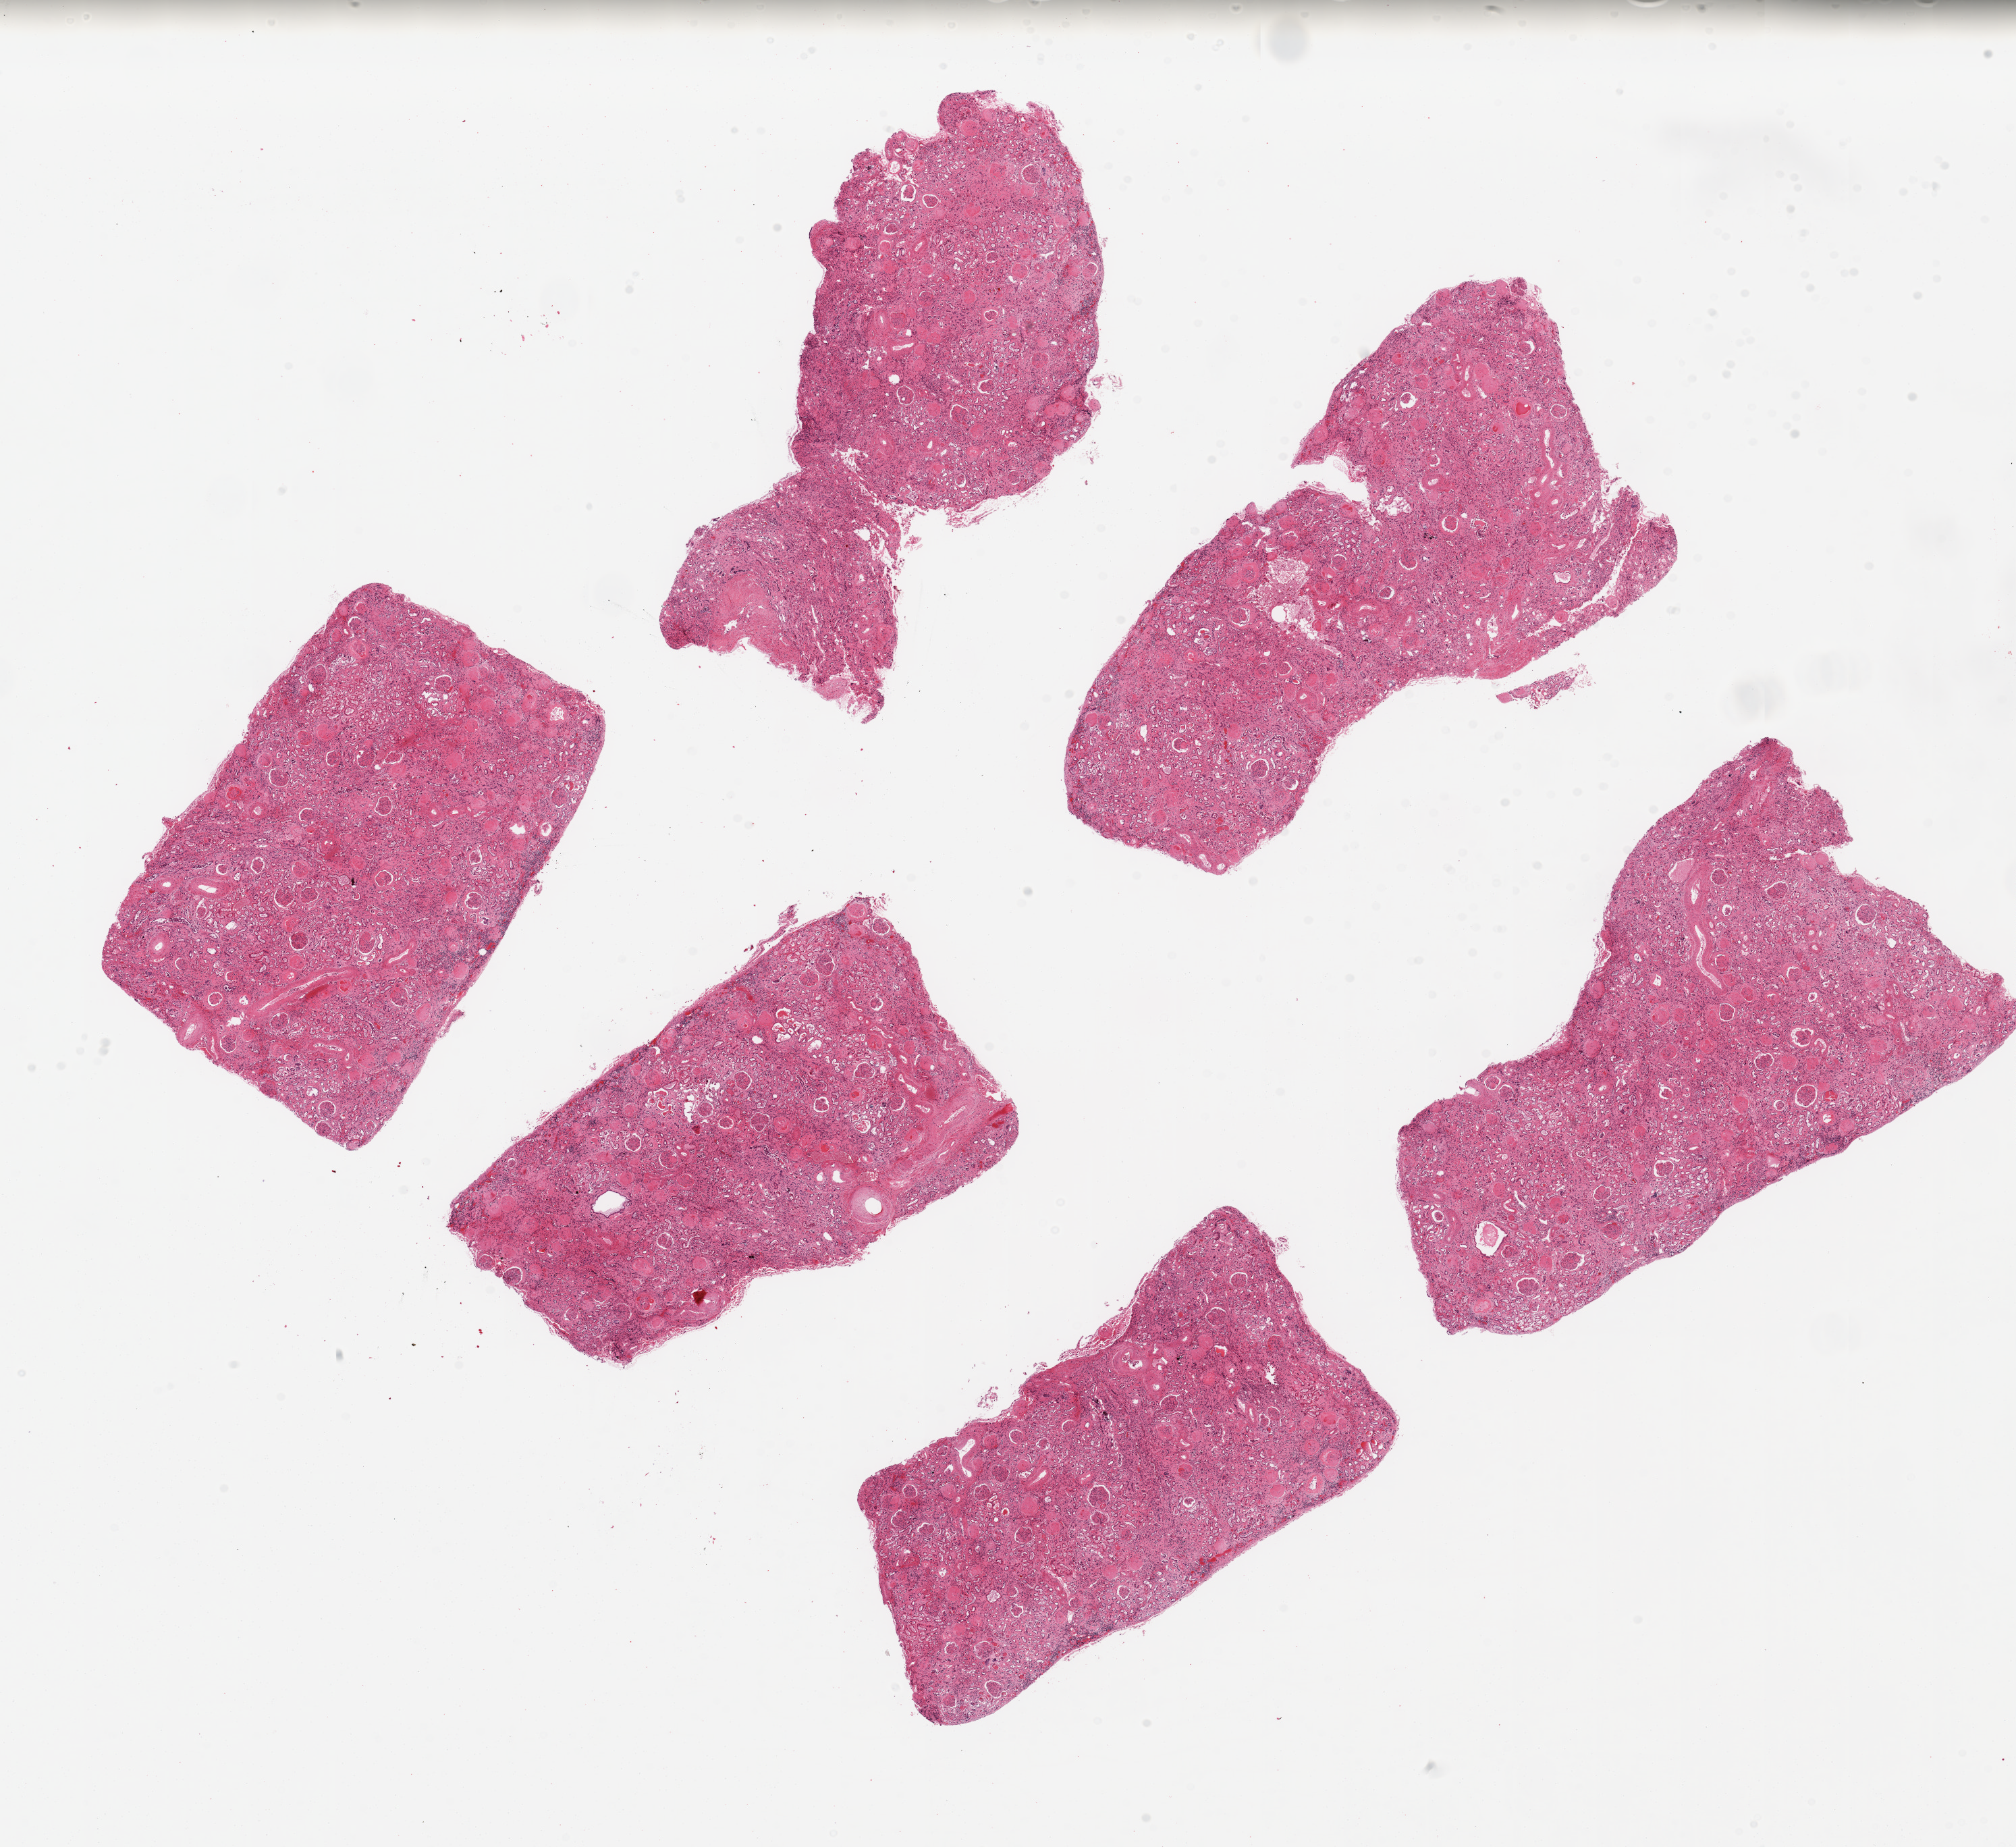
Whole-slide image, haematoxylin and eosin stain, brightfield — a low-resolution overview of the entire scanned area, about 23.6 x 21.6 mm, PAXgene-fixed, paraffin-embedded tissue, target tissue: renal cortex, tissue donor sample. Donor: female.
Reviewer comment on this tissue sample: 6 ~6x4mm pieces, tubules badly autolyzed.